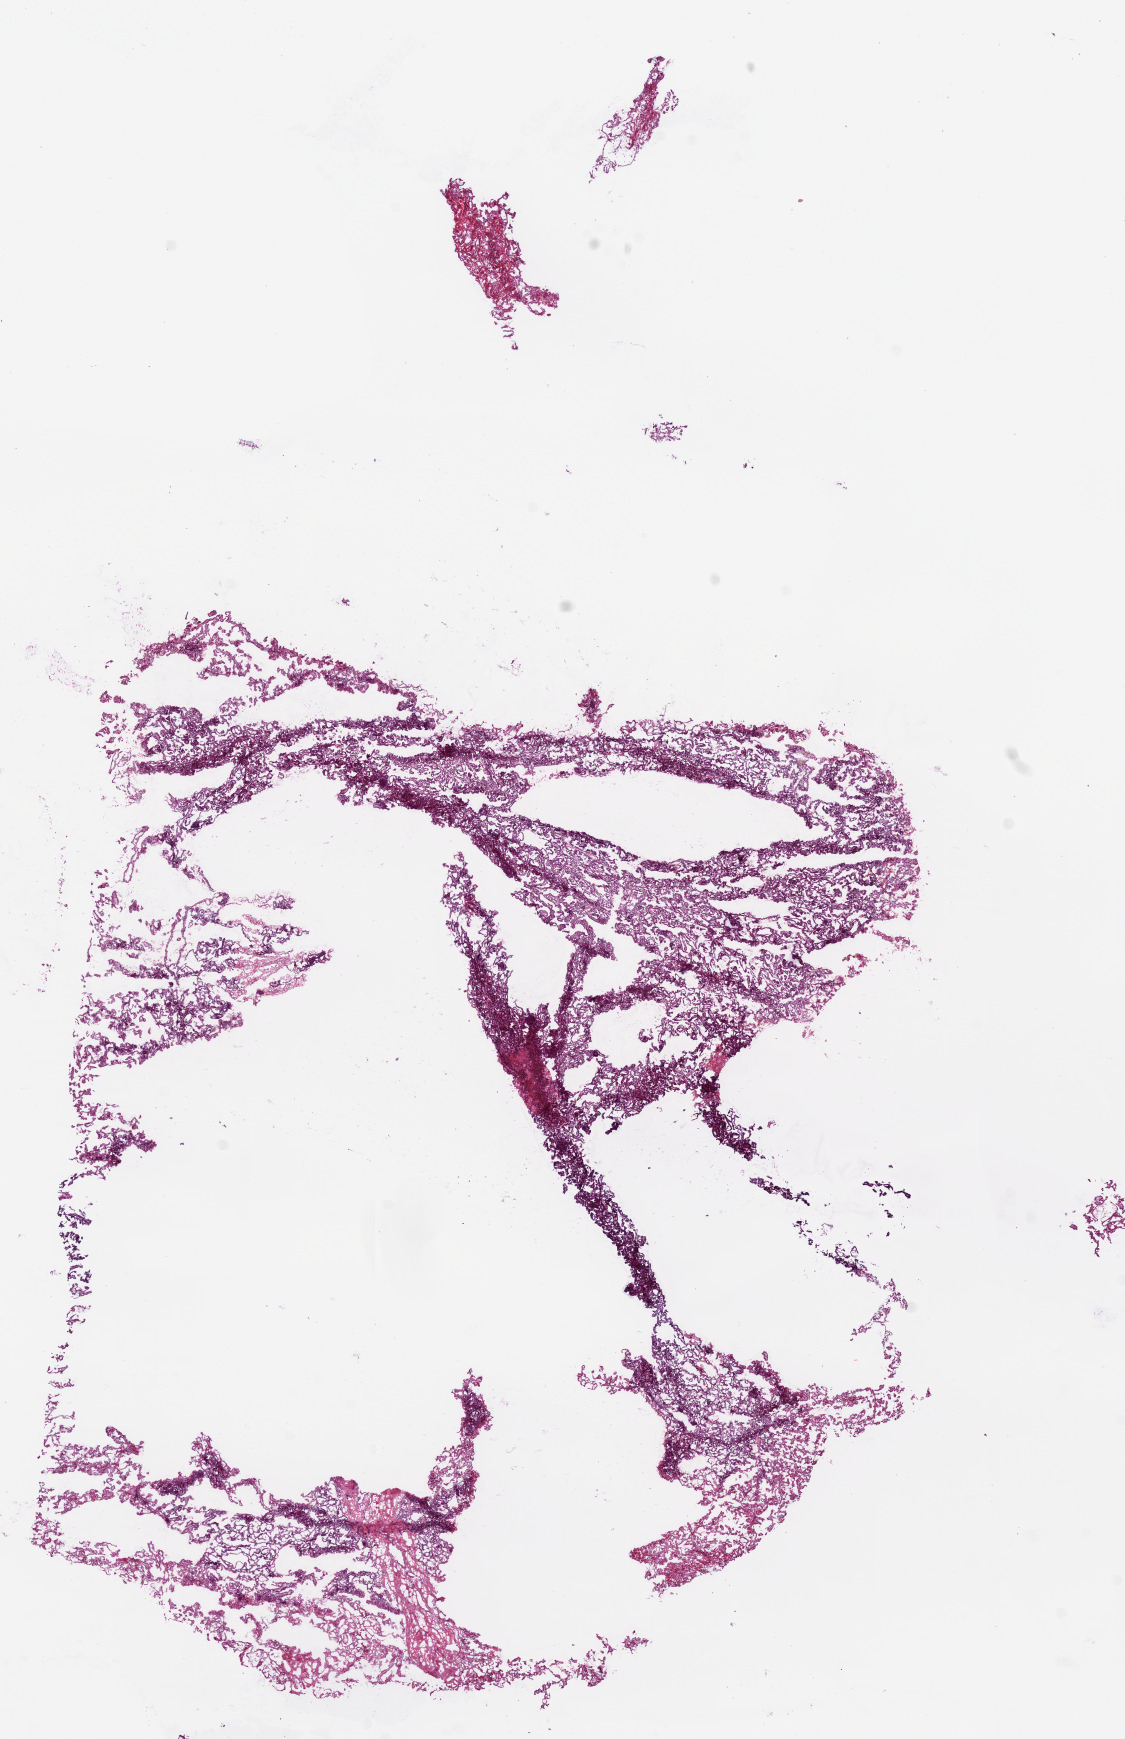
Hematoxylin and eosin (H&E) stained whole-slide image, whole scanned area (about 9.0 x 14.0 mm, slide scanned at 20x) shown as a low-resolution overview. Frozen section. Kidney, primary tumour sample. Male patient; age at initial diagnosis 74 years. Composition of this section per pathologist review: tumour cells 87%, tumour nuclei 80%, normal cells 0%, stromal cells 10%, necrosis 3%.
• histologic diagnosis: Papillary adenocarcinoma, NOS
• TNM: T1b NX M0
• AJCC pathologic stage: I